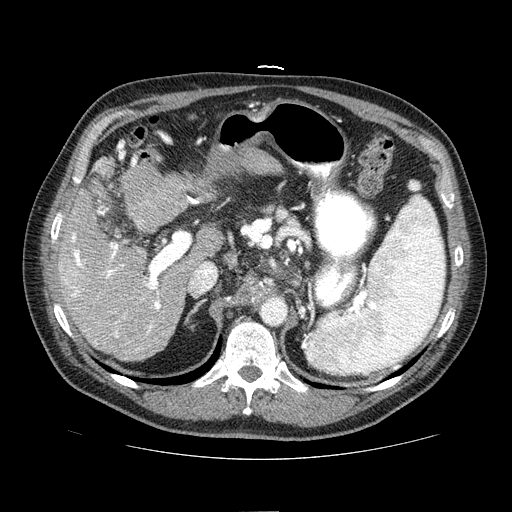
Contrast-enhanced abdominal CT (liver protocol), one axial slice. Slice 43 of 81 in the series (ordered by position). 100 kVp. One of 2 acquisitions stored at this slice position. Soft-tissue window (W 400 / L 40 HU). 2.5 mm slice thickness. 512 × 512 image matrix. Case-level facts recorded for this patient, not image findings: diagnosis: hepatocellular carcinoma (patient treated with transarterial chemoembolisation; whether this scan precedes or follows treatment is not stated here); TNM stage (as recorded): Stage-IIIA; Child-Pugh class: A; tumour differentiation: well differentiated; tumour nodularity: multinodular.
Structures marked on this image (semi-automatic segmentation, software-assisted and operator-edited):
- liver parenchyma outside the tumour (the mass and vessels are separate outlines, so this box may not span the whole liver): bounding box <57,182,200,360> (left, top, right, bottom; pixels)
- liver vessels: <60,233,161,350>